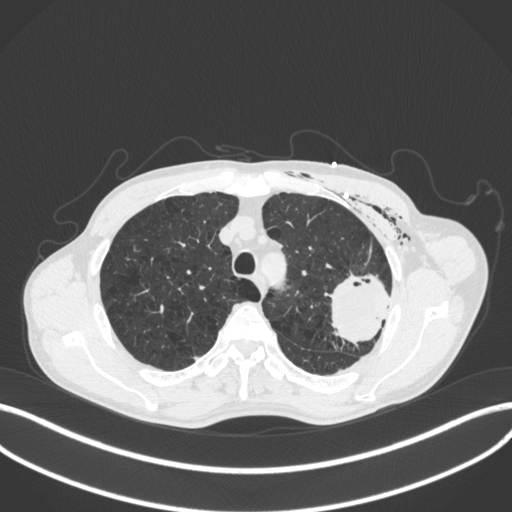
Chest CT, one axial slice. Slice 315 of 416 in the series (ordered by position). Lung window (W 1500 / L -600 HU). 1 mm slice thickness. 512 × 512 image matrix, field of view 400 × 400 mm. Male patient, age 58 years. From the clinical record (not read from this slice): clinical TNM (as recorded): T3 N0 M0.
Outlined on this slice (bounding box drawn by a radiologist):
- lung tumour (recorded histology: adenocarcinoma): bounding box [x1, y1, x2, y2] px = [327, 270, 401, 347]